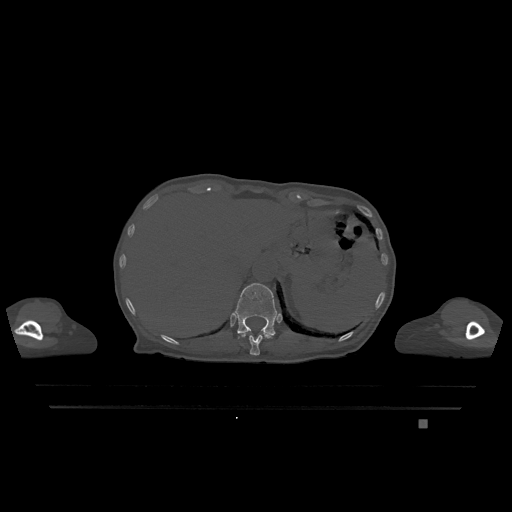
CT including the spine, one axial slice; position 553 of 1317 along the scan axis; bone window (W 1800 / L 400 HU); 0.5 mm slice thickness; 512 × 512 image matrix, field of view 500 × 500 mm. Female patient, age 74 years. From the clinical record (not read from this slice): primary cancer: lung.
Outlined on this slice (semi-automatically segmented with operator editing):
- T11 vertebra: bounding box [x1, y1, x2, y2] px = [240, 333, 273, 356]
- T12 vertebra: [235, 283, 278, 338]